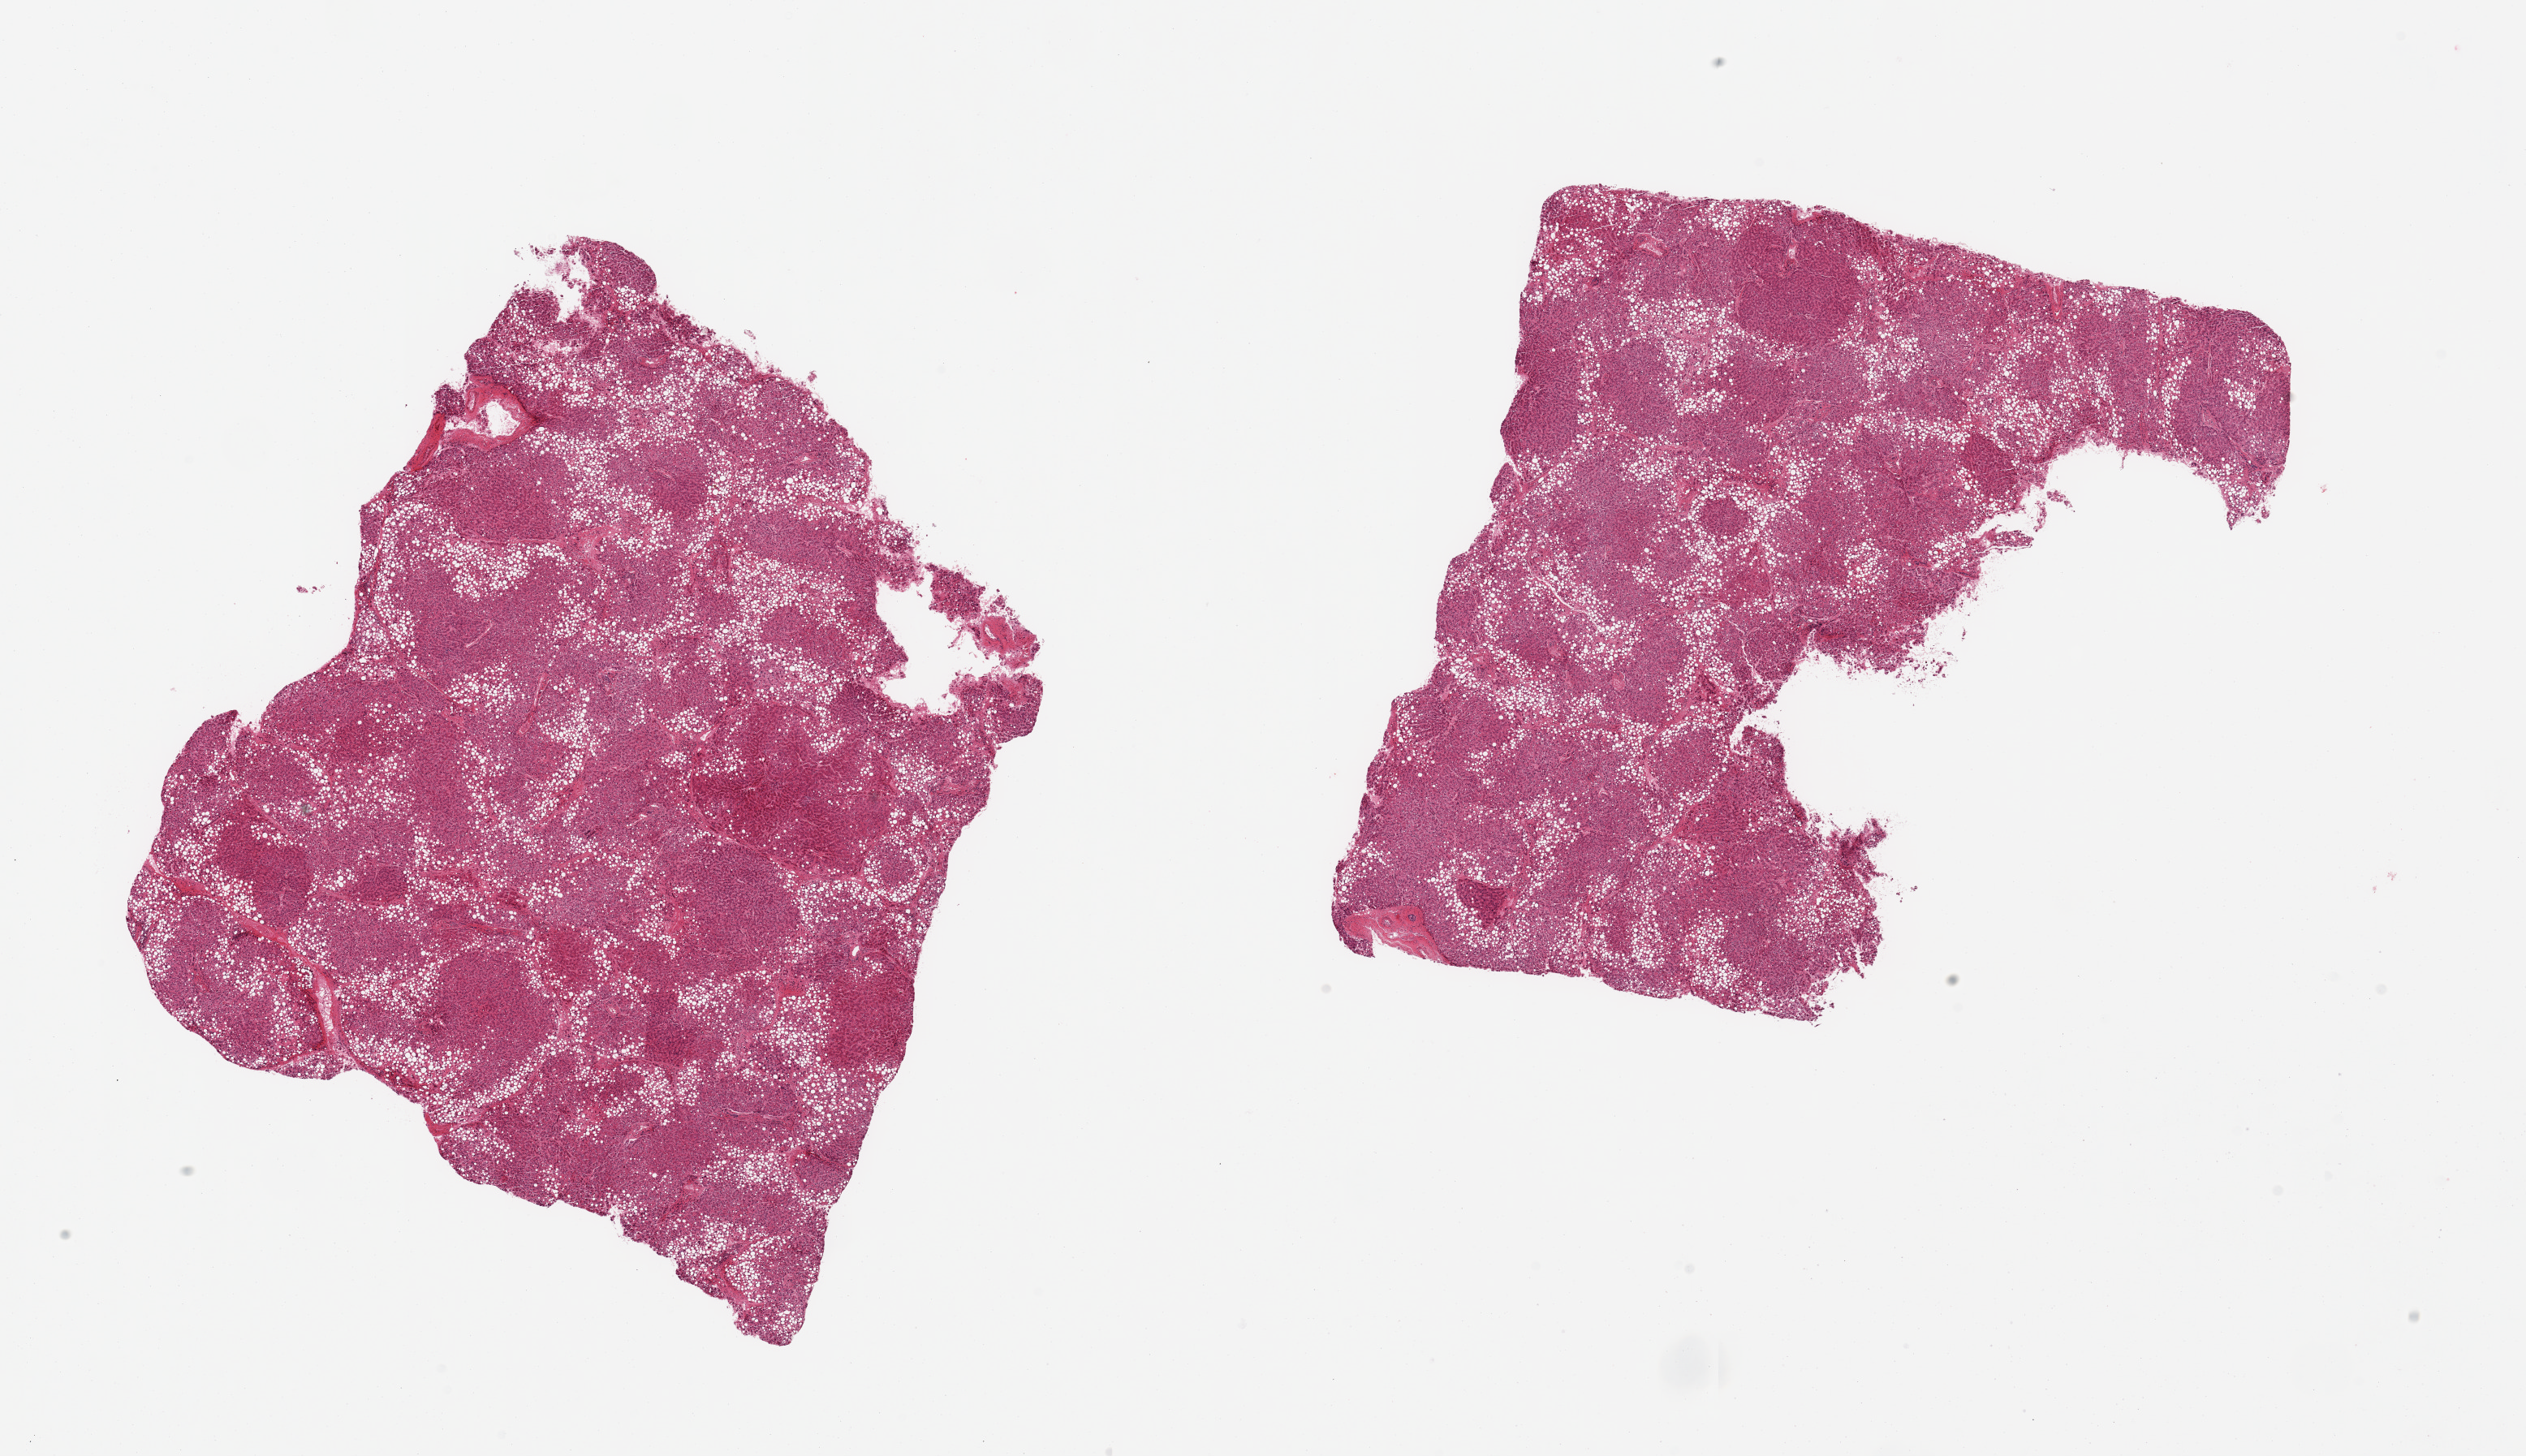
Whole-slide image, hematoxylin and eosin (H&E) stain — a low-resolution overview of the entire scanned area, about 24.6 x 14.2 mm (from a 20x scan); PAXgene-fixed paraffin-embedded (PFPE) section; sampled site (target tissue): liver; donor tissue sample. Male donor.
• reviewer comment on this tissue sample: 2 pieces; moderate (40%) macrovesicular steatosis; bridging fibrosis